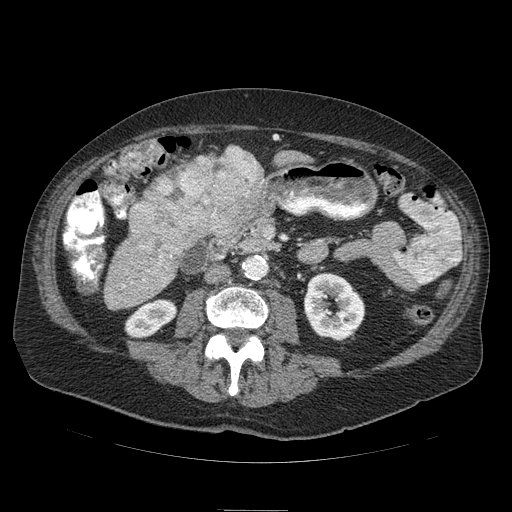
Contrast-enhanced abdominal CT (liver protocol), one axial slice; 120 kVp; soft-tissue window (W 400 / L 40 HU); 2.5 mm slice thickness; 512 × 512 image matrix, field of view 440 × 440 mm. From the clinical record (not read from this slice): diagnosis: hepatocellular carcinoma (patient treated with transarterial chemoembolisation; whether this scan precedes or follows treatment is not stated here); TNM stage (as recorded): Stage-IIIA.
Annotated regions visible in this slice (semi-automatic segmentation, software-assisted and operator-edited):
- liver parenchyma outside the tumour (the mass and vessels are separate outlines, so this box may not span the whole liver): bounding box [x1, y1, x2, y2] px = [238, 146, 307, 164]
- mass: [125, 145, 274, 269]